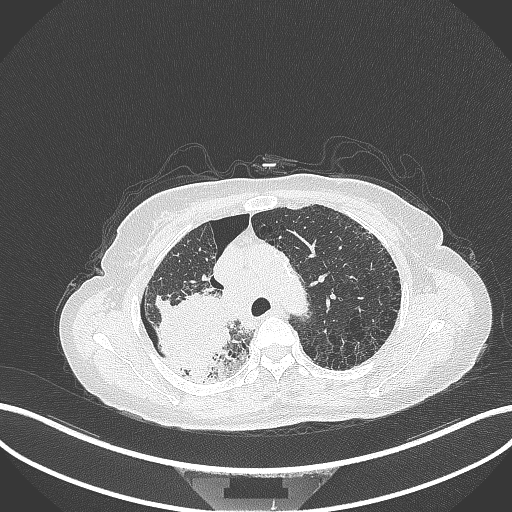
Chest CT, one axial slice. Position 258 of 408 along the scan axis. Reconstruction kernel B70f. 120 kVp. Lung window (W 1500 / L -600 HU). 1 mm slice thickness. 512 × 512 image matrix. Patient: female, 64 years. From the clinical record (not read from this slice): clinical TNM (as recorded): T3 N3 M0.
Structures marked on this image (bounding box drawn by a radiologist):
- lung tumour (recorded histology: squamous cell carcinoma): box from (x=147, y=284) to (x=235, y=385) px